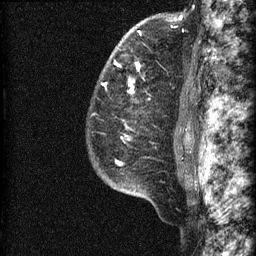
Breast MRI (dynamic contrast-enhanced), one sagittal slice. Position 51 of 60 along the scan axis. Dynamic contrast-enhanced series, image 2 of 3 at this slice position (ordered by acquisition). 1.5 T. TE 4.2 ms, TR 22.7 ms. 1.5 mm slice thickness. 256 × 256 image matrix, field of view 180 × 180 mm. Patient: female, 48 years. Case-level facts recorded for this patient, not image findings: setting: breast cancer imaged before/during neoadjuvant chemotherapy; receptor status: triple-negative.
Annotated regions visible in this slice (semi-automatically segmented with operator editing):
- analysis volume of interest (the breast-tissue region the enhancement analysis was run in; not a lesion): bounding box (x1, y1, x2, y2) in pixels: (85, 23, 186, 202)
- tumour enhancement mask (voxels above the 90 % enhancement threshold inside the analysis volume of interest): (102, 61, 141, 165)